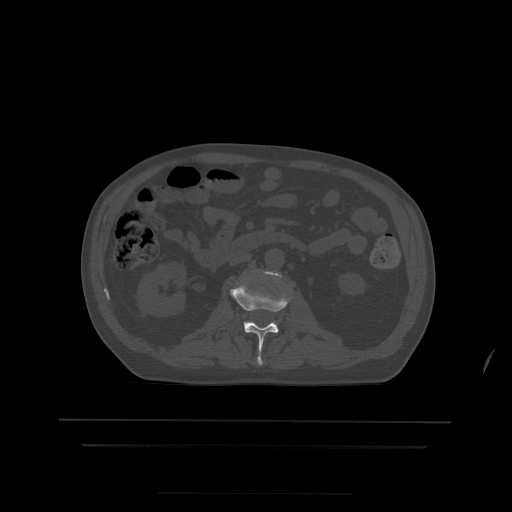
CT including the spine, one axial slice. Position 140 of 522 along the scan axis. Bone window (W 1800 / L 400 HU). 1.25 mm slice thickness. 512 × 512 image matrix, field of view 436 × 436 mm. Patient age 68 years. From the clinical record (not read from this slice): primary cancer: urothelial.
Outlined on this slice (semi-automatically segmented with operator editing):
- L2 vertebra: bounding box (x1, y1, x2, y2) in pixels: (230, 284, 291, 365)
- L3 vertebra: (264, 271, 281, 277)